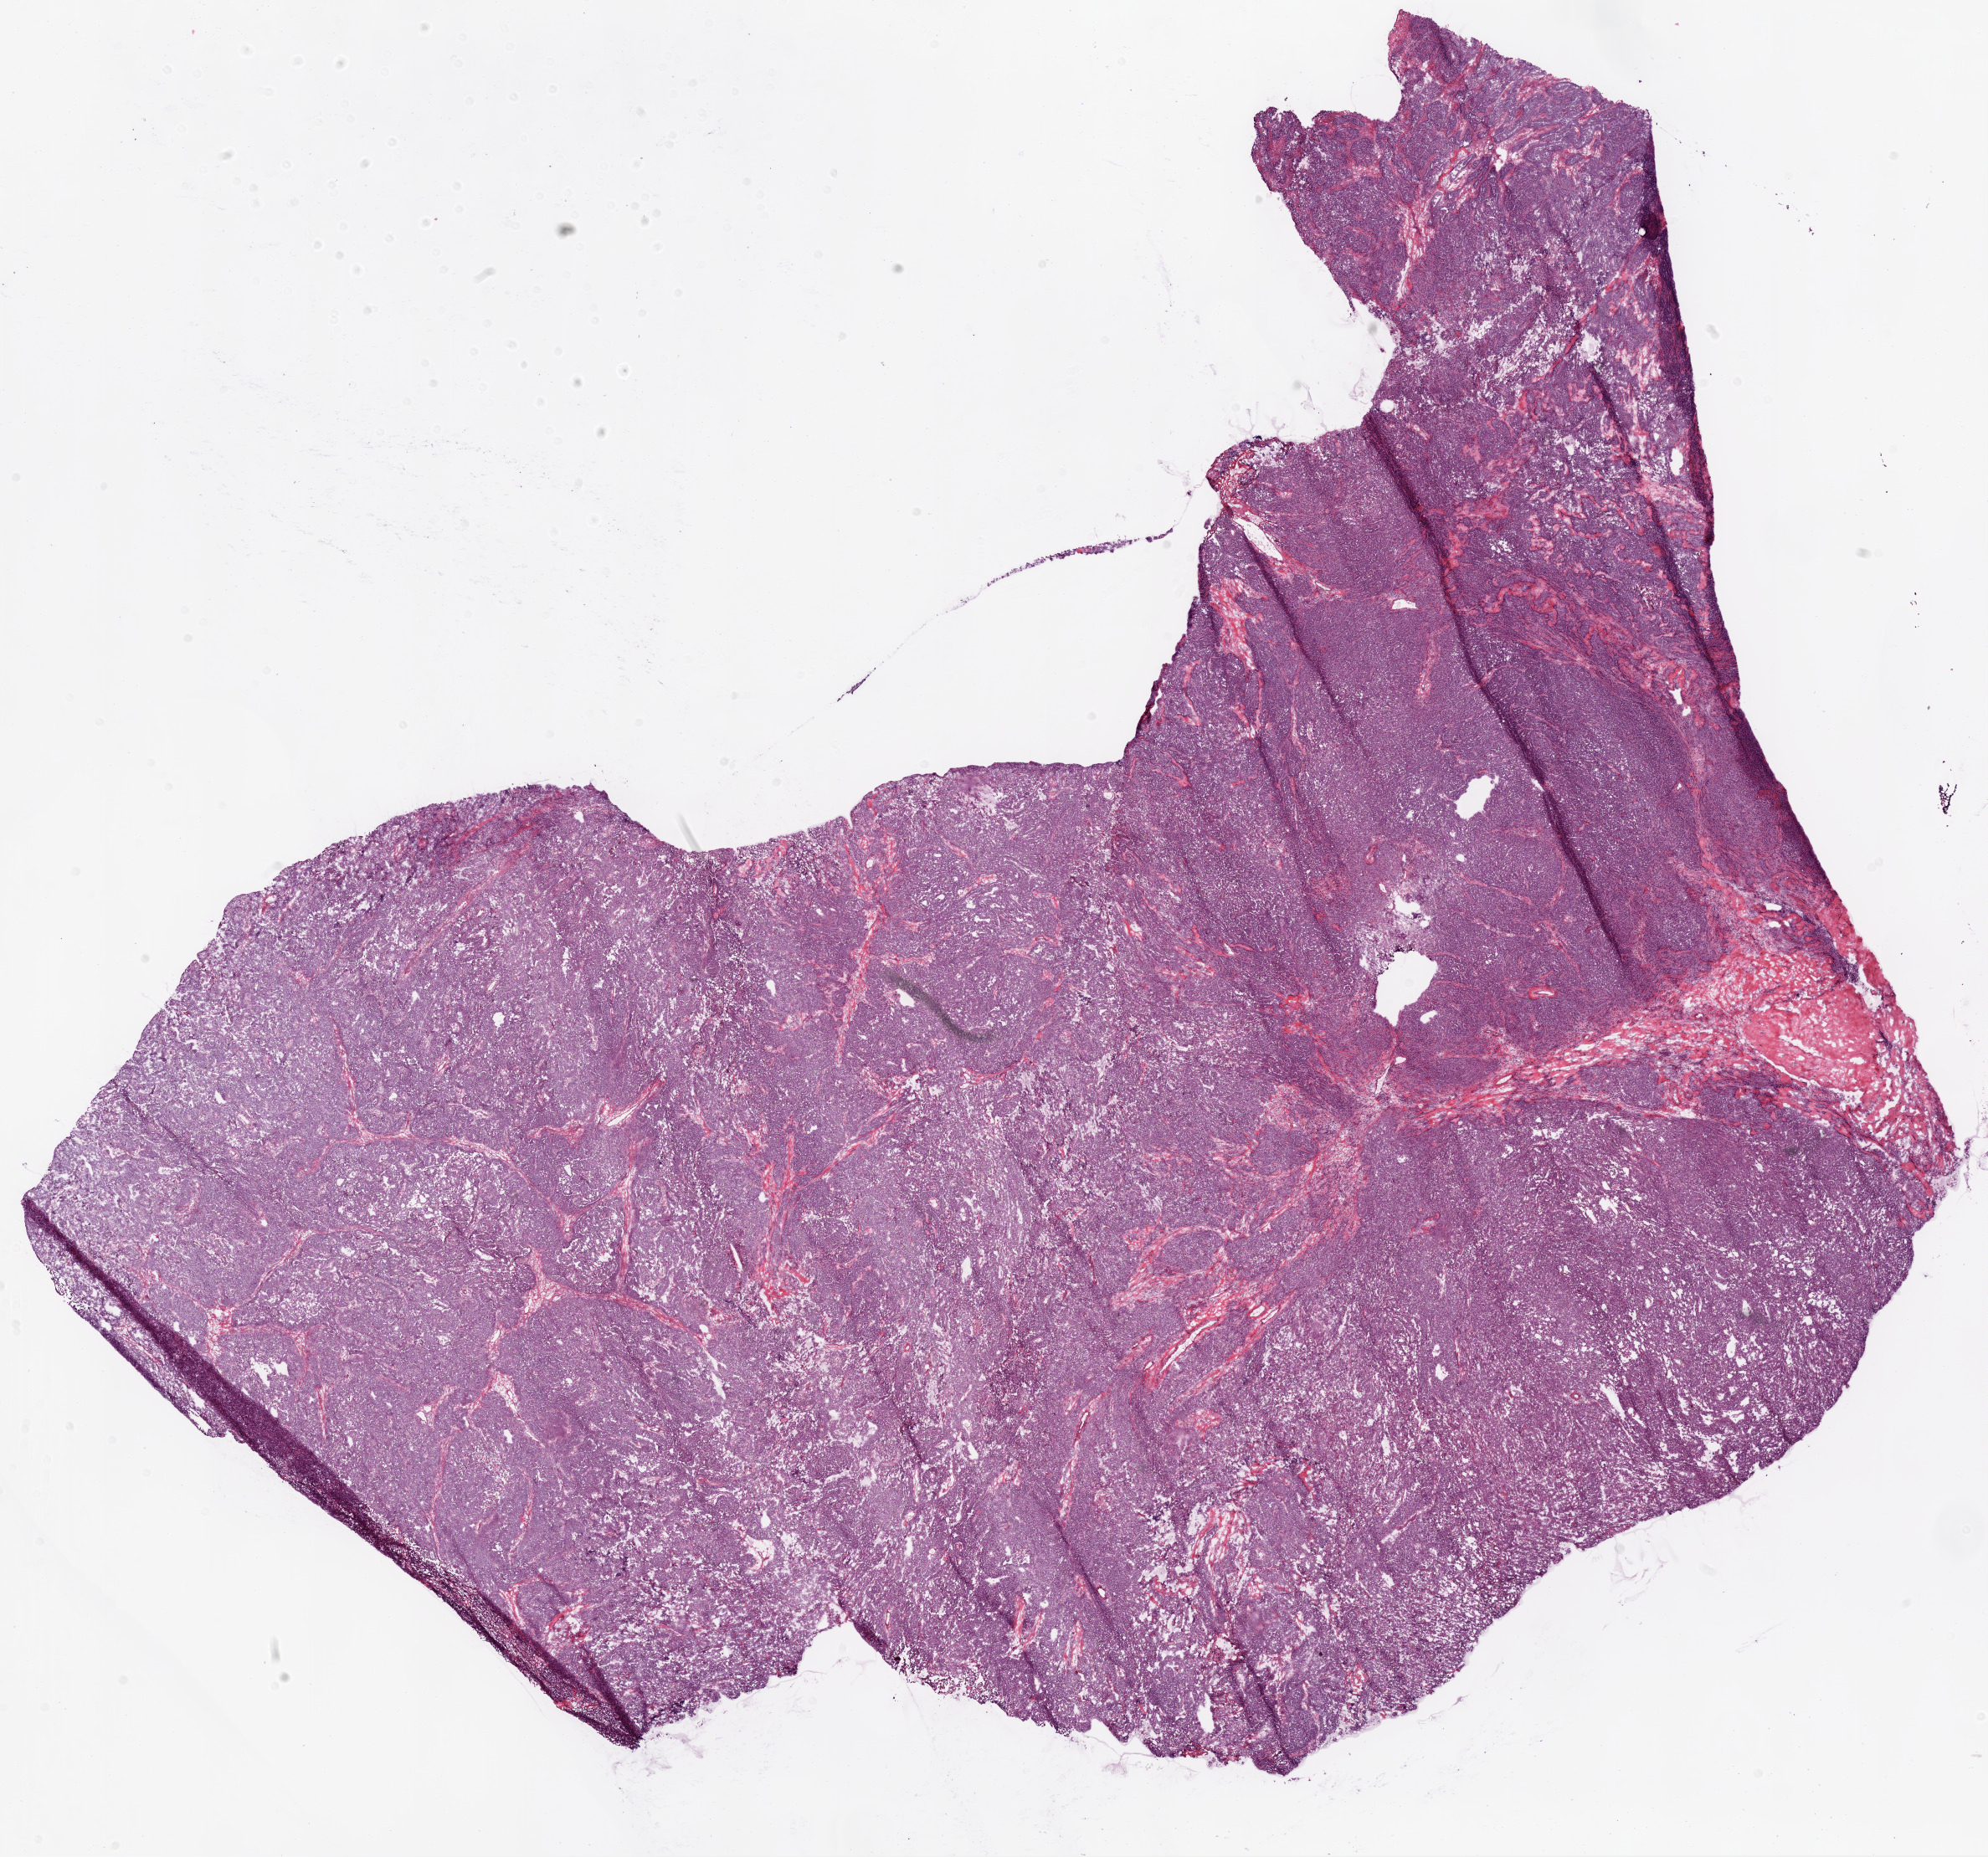
Whole-slide histology image, Hematoxylin and eosin (H&E) stained, whole scanned area (about 19.1 x 17.8 mm) shown as a low-resolution overview. Frozen section from the bottom of the tissue portion. Primary tumour sample from the ovary. Female patient; age at initial diagnosis 76 years. Histologic grade: G3 (poorly differentiated). Pathologist review of this section (percent, as recorded): tumour cells 95%, tumour nuclei 90%, normal cells 0%, stromal cells 0%, necrosis 5%. Infiltration values recorded for this section: lymphocyte infiltration 5%.
Pathologic diagnosis: Serous cystadenocarcinoma, NOS. FIGO stage: IIIB.